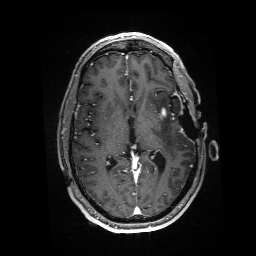
Brain MRI from a brain-tumour surgery series, one axial slice; position 85 of 176 along the scan axis; T1-weighted post-contrast; 1 mm slice thickness; 256 × 256 image matrix. Case-level facts recorded for this patient, not image findings: histopathology: Glioblastoma; WHO grade: 4; IDH mutation: no; tumour location: Left Anterior/Superior Temporal.
Annotated regions visible in this slice (expert manual segmentation):
- residual tumour: bounding box (x1, y1, x2, y2) in pixels: (160, 108, 167, 117)